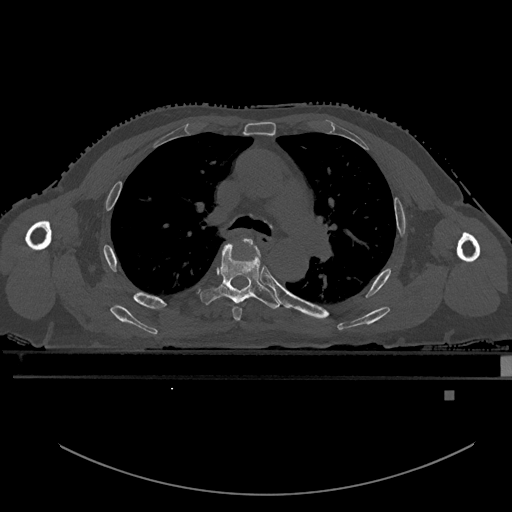
CT including the spine, one axial slice; slice 369 of 969 in the series (ordered by position); bone window (W 1800 / L 400 HU); 0.5 mm slice thickness; 512 × 512 image matrix, field of view 456 × 456 mm. Male patient, age 82 years. Case-level facts recorded for this patient, not image findings: primary cancer: prostate.
Annotated regions visible in this slice (semi-automatic segmentation, software-assisted and operator-edited):
- T4 vertebra: bounding box <232,237,260,321> (left, top, right, bottom; pixels)
- T5 vertebra: <201,242,280,310>